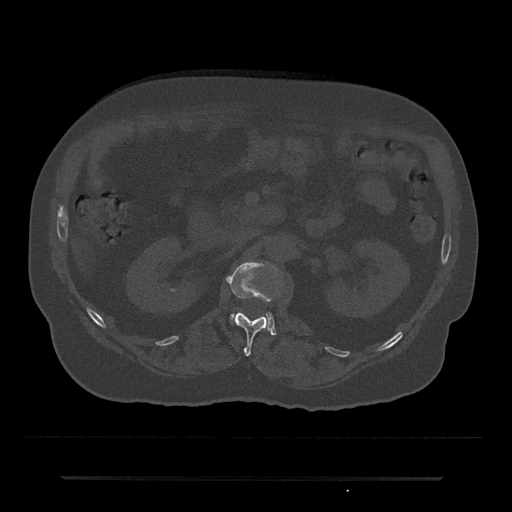
CT including the spine, one axial slice; position 52 of 797 along the scan axis; reconstruction kernel Br40s/3; bone window (W 1800 / L 400 HU); 0.5 mm slice thickness; 512 × 512 image matrix, field of view 437 × 437 mm. Male patient, age 69 years. Case-level facts recorded for this patient, not image findings: primary cancer: prostate.
Outlined on this slice (semi-automatic segmentation, software-assisted and operator-edited):
- L1 vertebra: bounding box [x1, y1, x2, y2] px = [227, 261, 282, 356]
- L2 vertebra: [230, 312, 276, 335]